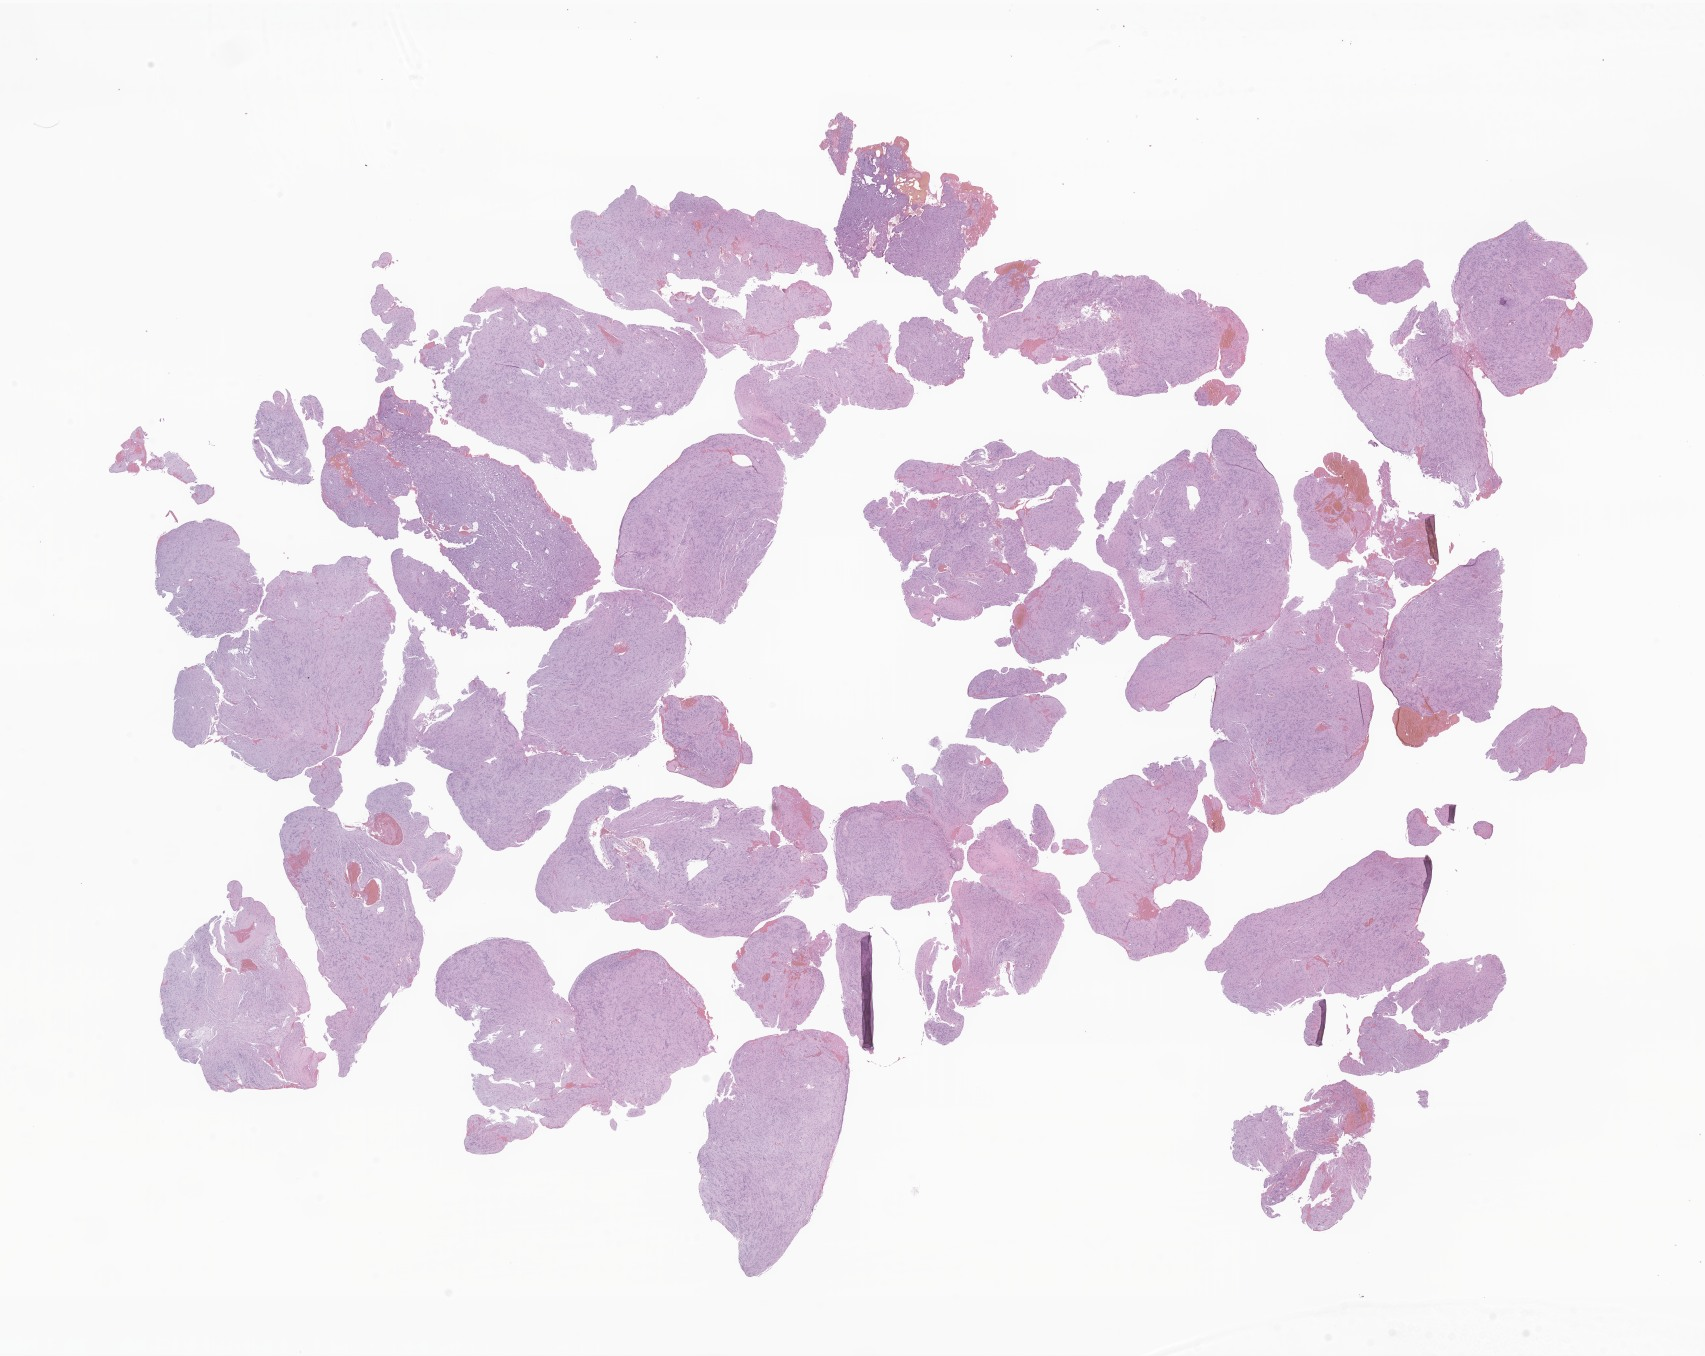
Whole-slide image, haematoxylin and eosin stain of tumor tissue from the brain — low-resolution overview of the scanned area, about 28.8 x 22.9 mm. Formalin-fixed, paraffin-embedded (FFPE) tissue. Male patient, age 186 months (15 years 6 months).
Diagnosis (ICD-O-3 morphology term): Tumor cells, benign.